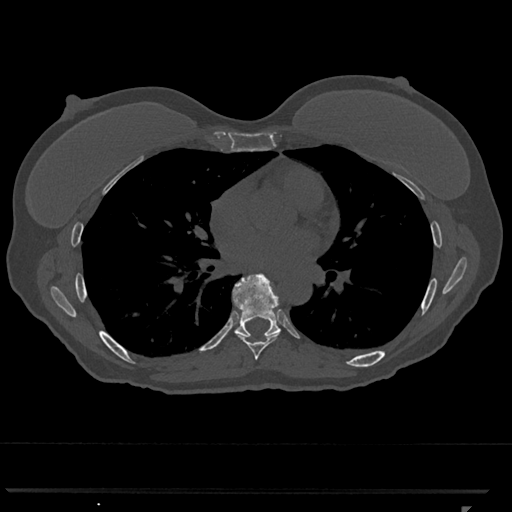
CT including the spine, one axial slice; slice 691 of 793 in the series (ordered by position); bone window (W 1800 / L 400 HU); 512 × 512 image matrix, field of view 380 × 380 mm. Female patient, age 62 years. Case-level facts recorded for this patient, not image findings: primary cancer: renal.
Outlined on this slice (semi-automatically segmented with operator editing):
- T7 vertebra: bounding box <234,331,281,360> (left, top, right, bottom; pixels)
- T8 vertebra: <233,273,281,337>